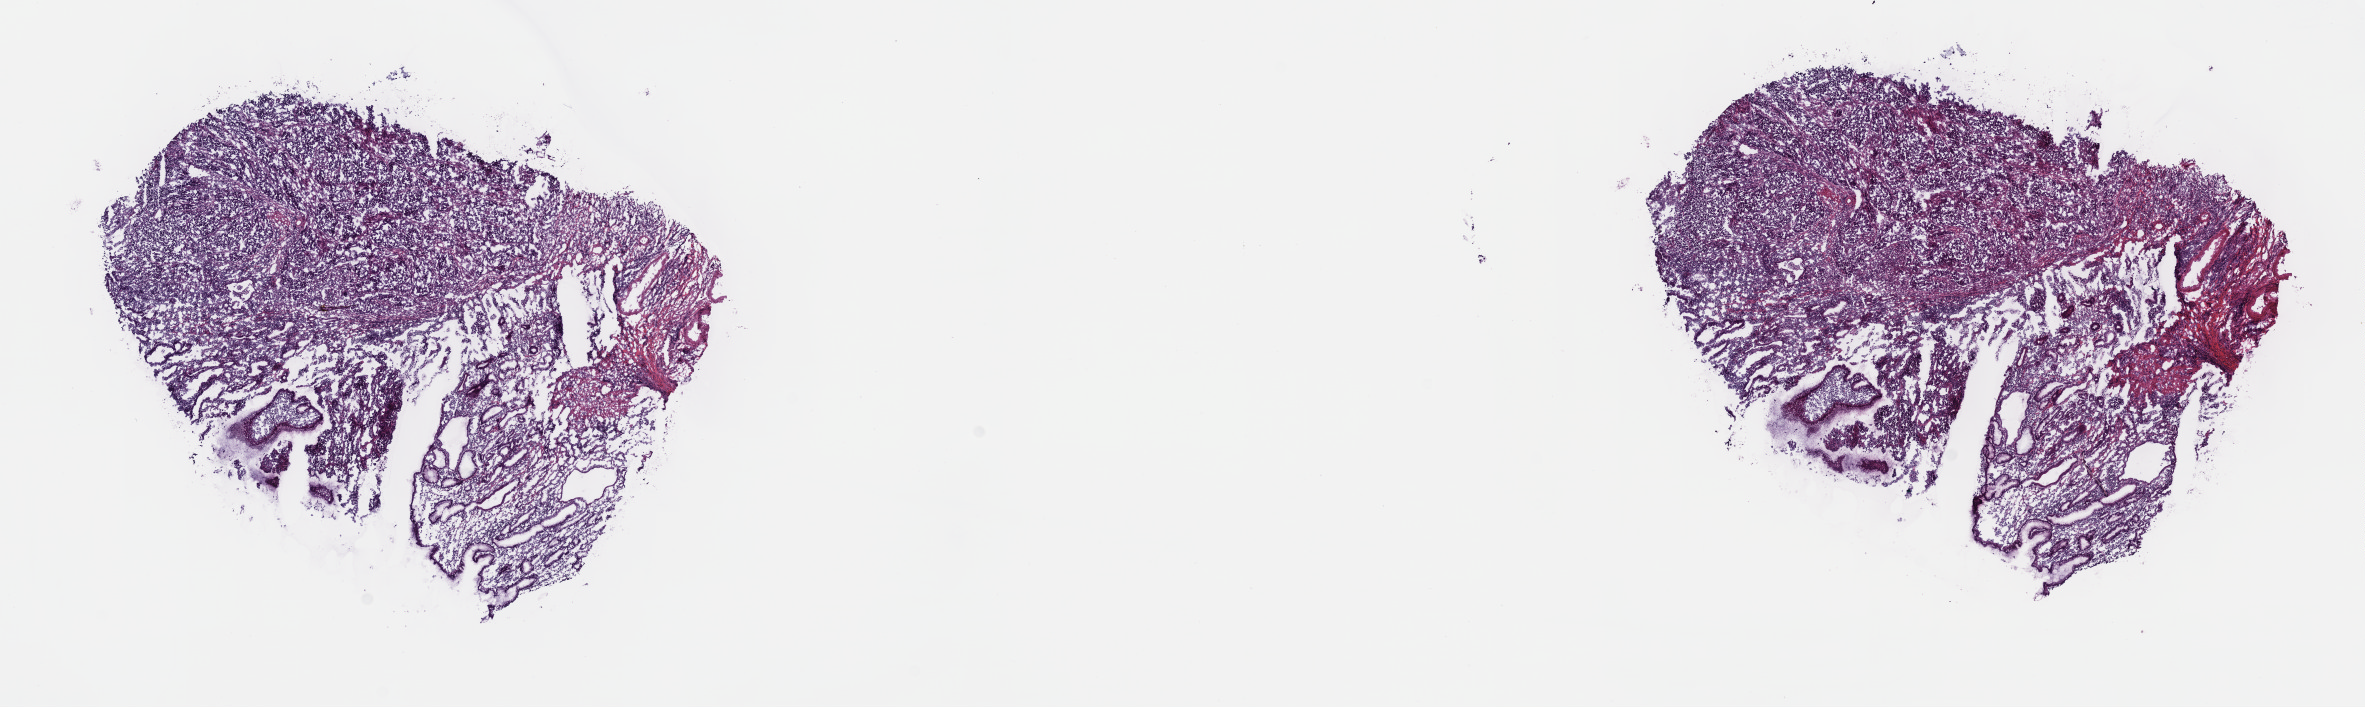
Whole-slide histology image, Hematoxylin and eosin (H&E) stained — shown as a low-resolution overview of the whole scanned area (about 19.1 x 5.7 mm, acquisition: 40x scan). Frozen section from the top of the tissue portion. Primary tumour sample from the stomach. Male, age 75 years at initial diagnosis. Pathologist review of this section (percent, as recorded): tumour cells 60%, tumour nuclei 60%.
Diagnosis: Adenocarcinoma, intestinal type.